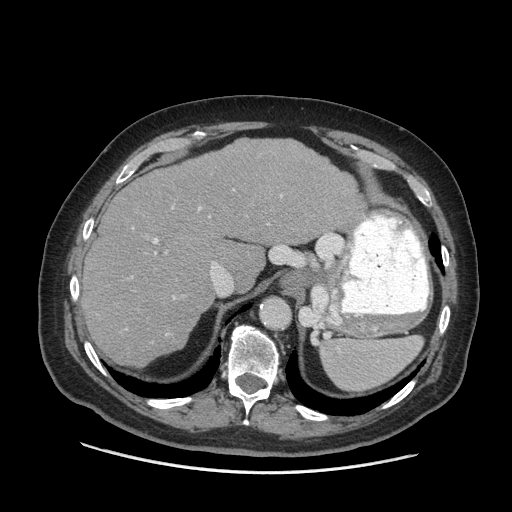
Contrast-enhanced abdominal CT (liver protocol), one axial slice; slice 50 of 77 in the series (ordered by position); reconstruction kernel STANDARD; 140 kVp; soft-tissue window (W 400 / L 40 HU); 2.5 mm slice thickness; 512 × 512 image matrix, field of view 420 × 420 mm. From the clinical record (not read from this slice): diagnosis: hepatocellular carcinoma (patient treated with transarterial chemoembolisation; whether this scan precedes or follows treatment is not stated here); TNM stage (as recorded): Stage-I; Child-Pugh class: A; tumour nodularity: uninodular; tumour size: 3.8 cm.
Structures marked on this image (semi-automatic segmentation, software-assisted and operator-edited):
- liver parenchyma outside the tumour (the mass and vessels are separate outlines, so this box may not span the whole liver): bounding box [x1, y1, x2, y2] px = [82, 139, 364, 366]
- liver vessels: [153, 189, 283, 335]